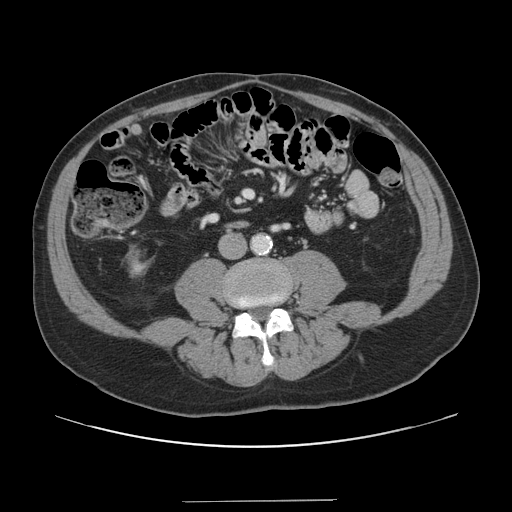
Contrast-enhanced abdominal CT, one axial slice. 120 kVp. Intravenous contrast given. Soft-tissue window (W 400 / L 40 HU). 2.5 mm slice thickness. 512 × 512 image matrix, field of view 399 × 399 mm. Male patient, age 63 years. Case-level facts recorded for this patient, not image findings: diagnosis: colorectal cancer liver metastases, imaged before liver resection.
Annotated regions visible in this slice (manually delineated by an expert):
- portal vein (with intrahepatic branches): box from (x=245, y=193) to (x=252, y=197) px